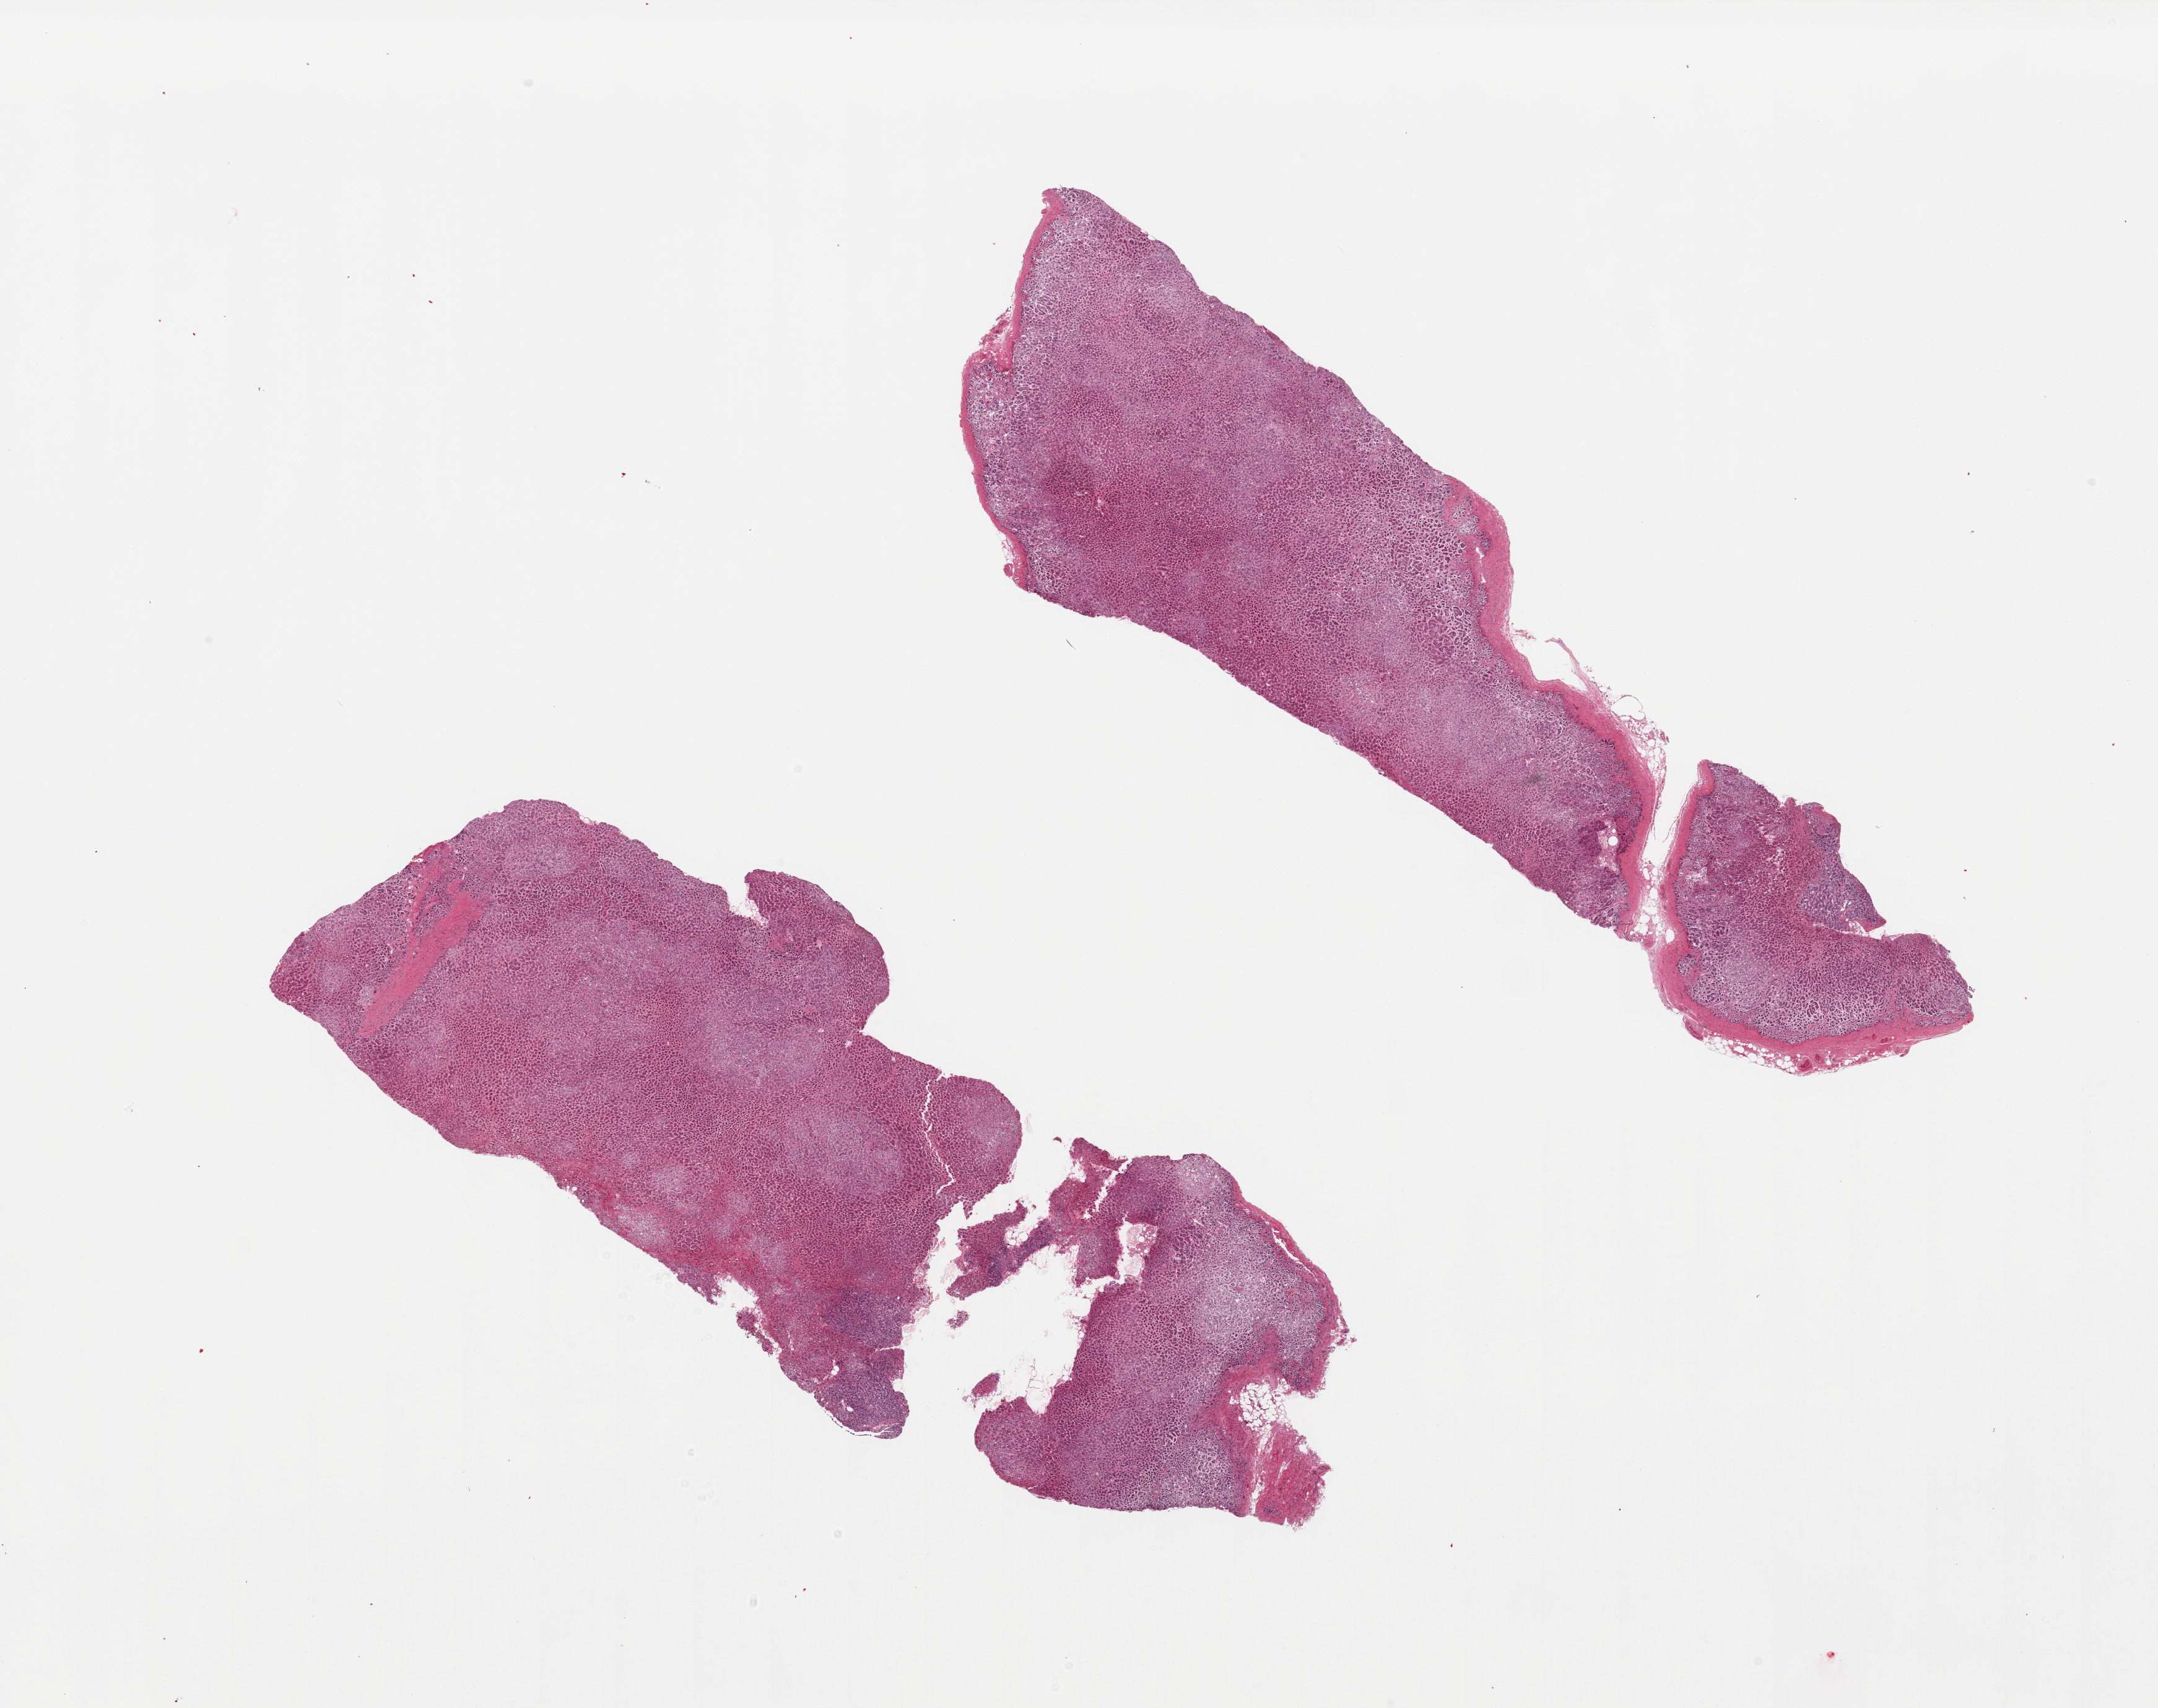
Hematoxylin and eosin (H&E) whole-slide image, brightfield — whole scanned area (about 27.6 x 21.8 mm, acquisition: 20x scan) shown as a low-resolution overview. PAXgene-fixed paraffin-embedded (PFPE) section. Section of adrenal gland (target tissue). Donor tissue sample. Donor: female.
Reviewer comment on this tissue sample: 2 pieces, all cortex.